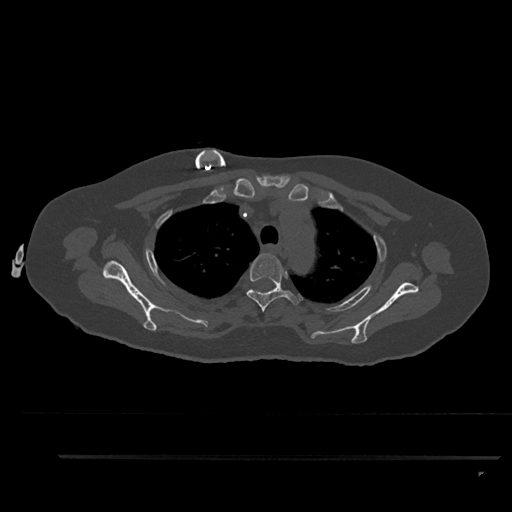
CT including the spine, one axial slice. Slice 683 of 797 in the series (ordered by position). Reconstruction kernel Br40s/3. 120 kVp. Bone window (W 1800 / L 400 HU). 512 × 512 image matrix, field of view 408 × 408 mm. Female patient, age 44 years. Case-level facts recorded for this patient, not image findings: primary cancer: renal; vertebrae with lytic lesions (as recorded): L1.
Structures marked on this image (semi-automatic segmentation, software-assisted and operator-edited):
- T3 vertebra: bounding box (x1, y1, x2, y2) in pixels: (246, 253, 298, 312)